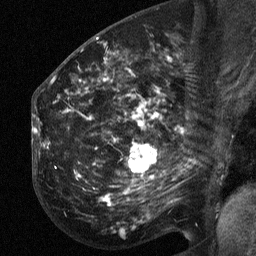
Breast MRI (dynamic contrast-enhanced), one sagittal slice. Slice 31 of 64 in the series (ordered by position). Dynamic contrast-enhanced study with each time point stored as its own series, time point 2 of 3 at this slice position (early post-contrast, ordered by acquisition time). 1.5 T. TE 4.8 ms, TR 27 ms. 2.3 mm slice thickness. 256 × 256 image matrix, field of view 200 × 200 mm. Patient: female, 50 years. From the clinical record (not read from this slice): setting: breast cancer imaged before/during neoadjuvant chemotherapy; receptor status: HER2-positive.
Annotated regions visible in this slice (semi-automatic segmentation, software-assisted and operator-edited):
- analysis volume of interest (the breast-tissue region the enhancement analysis was run in; not a lesion): bounding box [x1, y1, x2, y2] px = [54, 64, 205, 215]
- tumour enhancement mask (voxels above the 90 % enhancement threshold inside the analysis volume of interest): [125, 144, 156, 193]